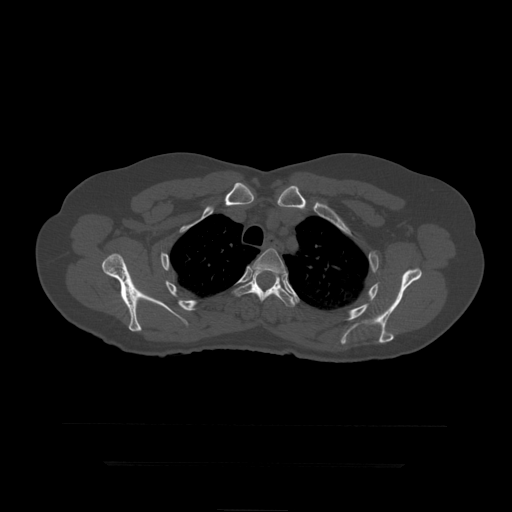
CT including the spine, one axial slice. Position 341 of 399 along the scan axis. 120 kVp. Bone window (W 1800 / L 400 HU). 1.25 mm slice thickness. 512 × 512 image matrix, field of view 450 × 450 mm. Patient age 41 years. Case-level facts recorded for this patient, not image findings: primary cancer: breast.
Outlined on this slice (semi-automatically segmented with operator editing):
- T4 vertebra: bounding box [x1, y1, x2, y2] px = [253, 249, 285, 290]
- T5 vertebra: [232, 270, 295, 307]